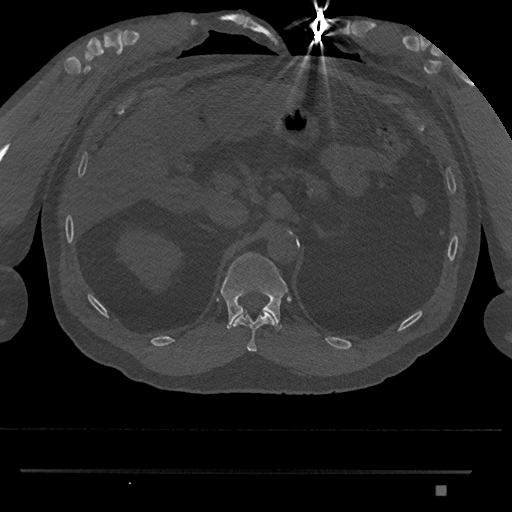
CT including the spine, one axial slice. Position 913 of 1134 along the scan axis. Reconstruction kernel Br40s/3. 120 kVp. Bone window (W 1800 / L 400 HU). 0.5 mm slice thickness. 512 × 512 image matrix, field of view 429 × 429 mm. Male patient, age 65 years. Case-level facts recorded for this patient, not image findings: primary cancer: prostate.
Annotated regions visible in this slice (semi-automatically segmented with operator editing):
- T11 vertebra: bounding box [x1, y1, x2, y2] px = [233, 312, 275, 352]
- T12 vertebra: [220, 252, 288, 331]